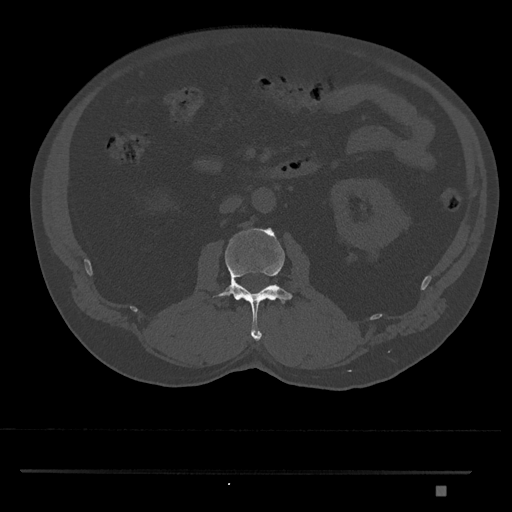
CT including the spine, one axial slice. Slice 748 of 1134 in the series (ordered by position). Reconstruction kernel Br40s/3. 120 kVp. Bone window (W 1800 / L 400 HU). 0.5 mm slice thickness. 512 × 512 image matrix, field of view 429 × 429 mm. Male patient, age 65 years. Case-level facts recorded for this patient, not image findings: primary cancer: prostate.
Structures marked on this image (semi-automatic segmentation, software-assisted and operator-edited):
- L2 vertebra: bounding box [x1, y1, x2, y2] px = [214, 228, 293, 341]